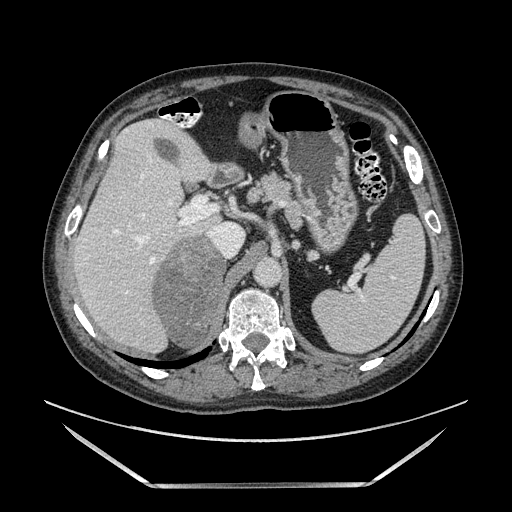
Contrast-enhanced abdominal CT, one axial slice; slice 97 of 185 in the series (ordered by position); soft-tissue window (W 400 / L 40 HU); 1.25 mm slice thickness; 512 × 512 image matrix, field of view 440 × 440 mm. Male patient. Case-level facts recorded for this patient, not image findings: diagnosis: adrenocortical carcinoma; tumour side: right adrenal; tumour size at pathology: 10.3 cm; Ki-67 index: 20 %; stage (as recorded): 3.
Outlined on this slice (semi-automatic segmentation, software-assisted and operator-edited):
- mass: bounding box <152,235,227,348> (left, top, right, bottom; pixels)